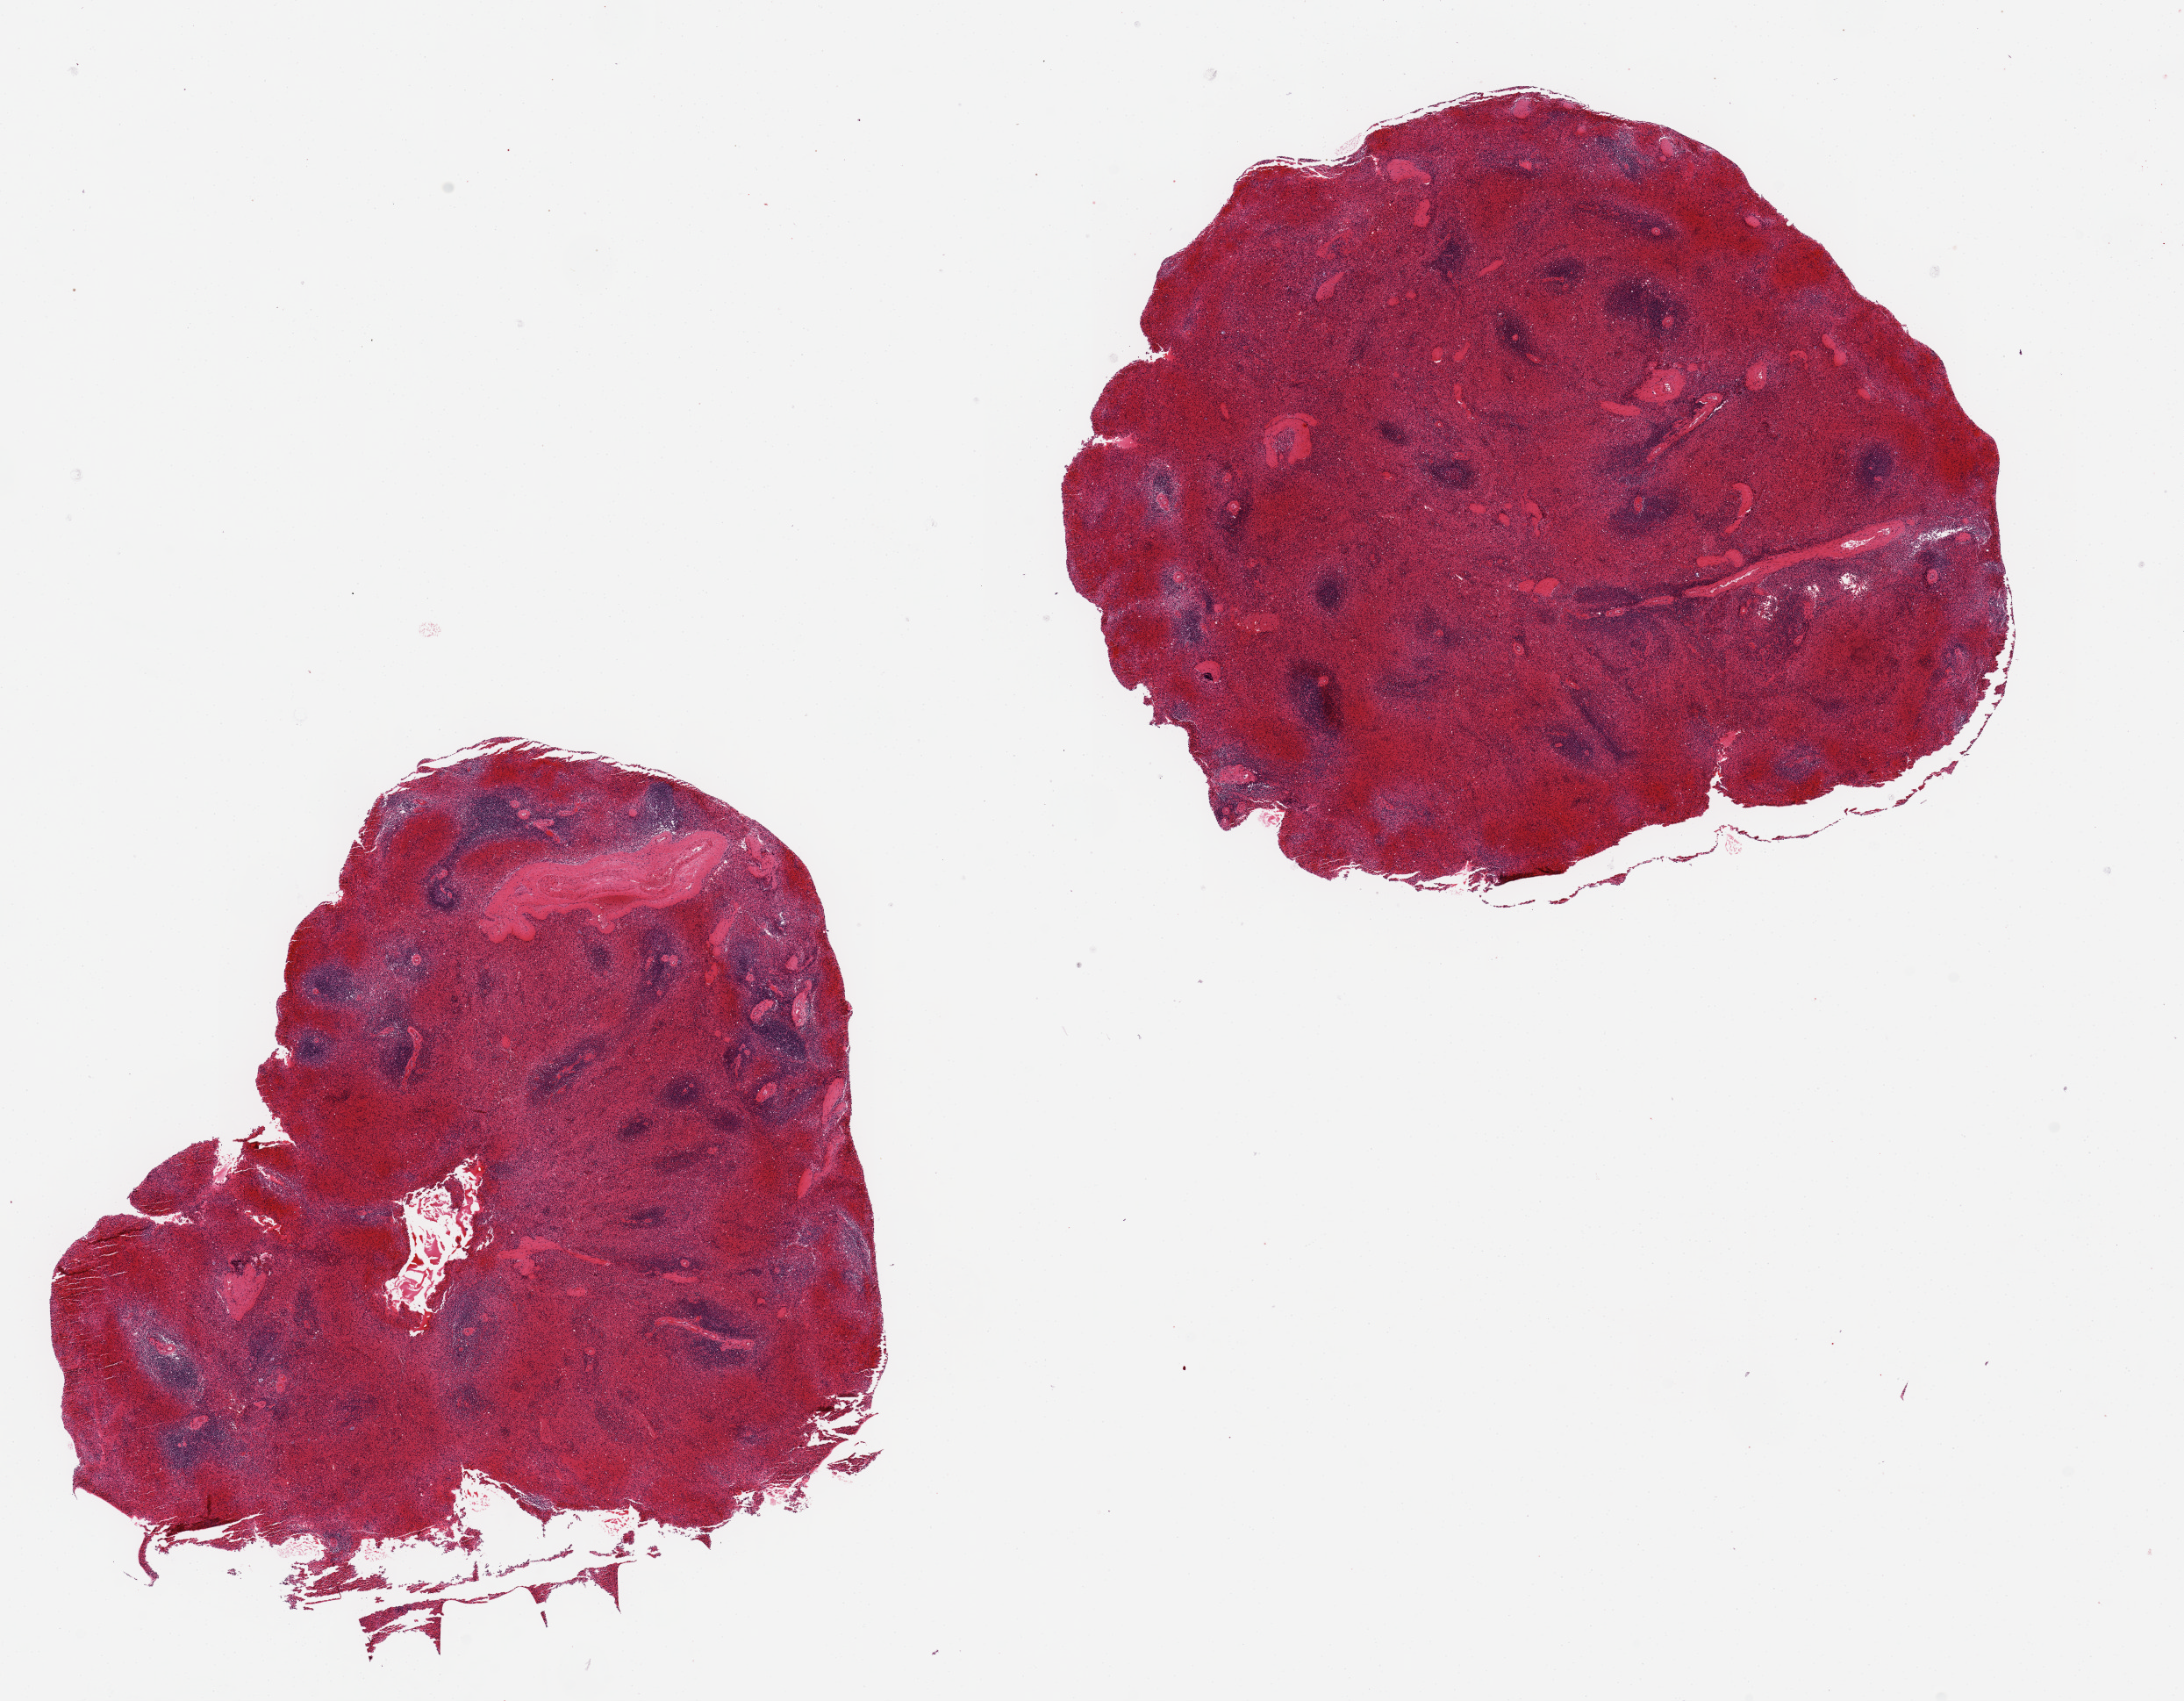
Digitized haematoxylin and eosin-stained section — whole scanned area (about 19.7 x 15.3 mm) shown as a low-resolution overview. PAXgene-fixed paraffin-embedded (PFPE) section. Section of spleen (target tissue). Tissue donor sample. Donor: female.
Review note (as recorded): 2 pieces, 8x7 & 8x7 mm; markedly congested.